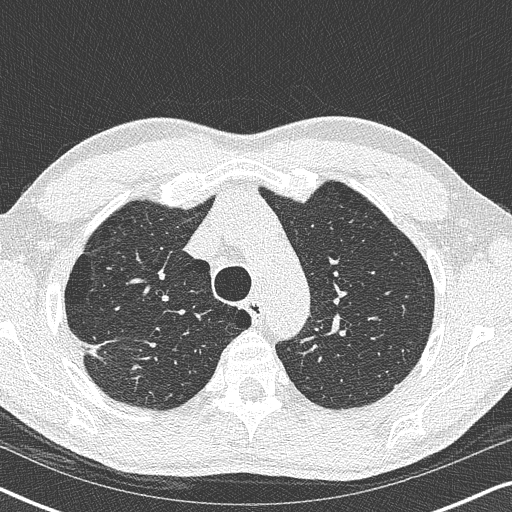
Low-dose screening chest CT, one axial slice; reconstruction kernel B50f; lung window (W 1500 / L -600 HU); 1 mm slice thickness; 512 × 512 image matrix, field of view 330 × 330 mm.
Structures marked on this image (manually delineated by an expert):
- lesion 1 (tumor, upper lobe of right lung): bounding box <81,340,98,354> (left, top, right, bottom; pixels)